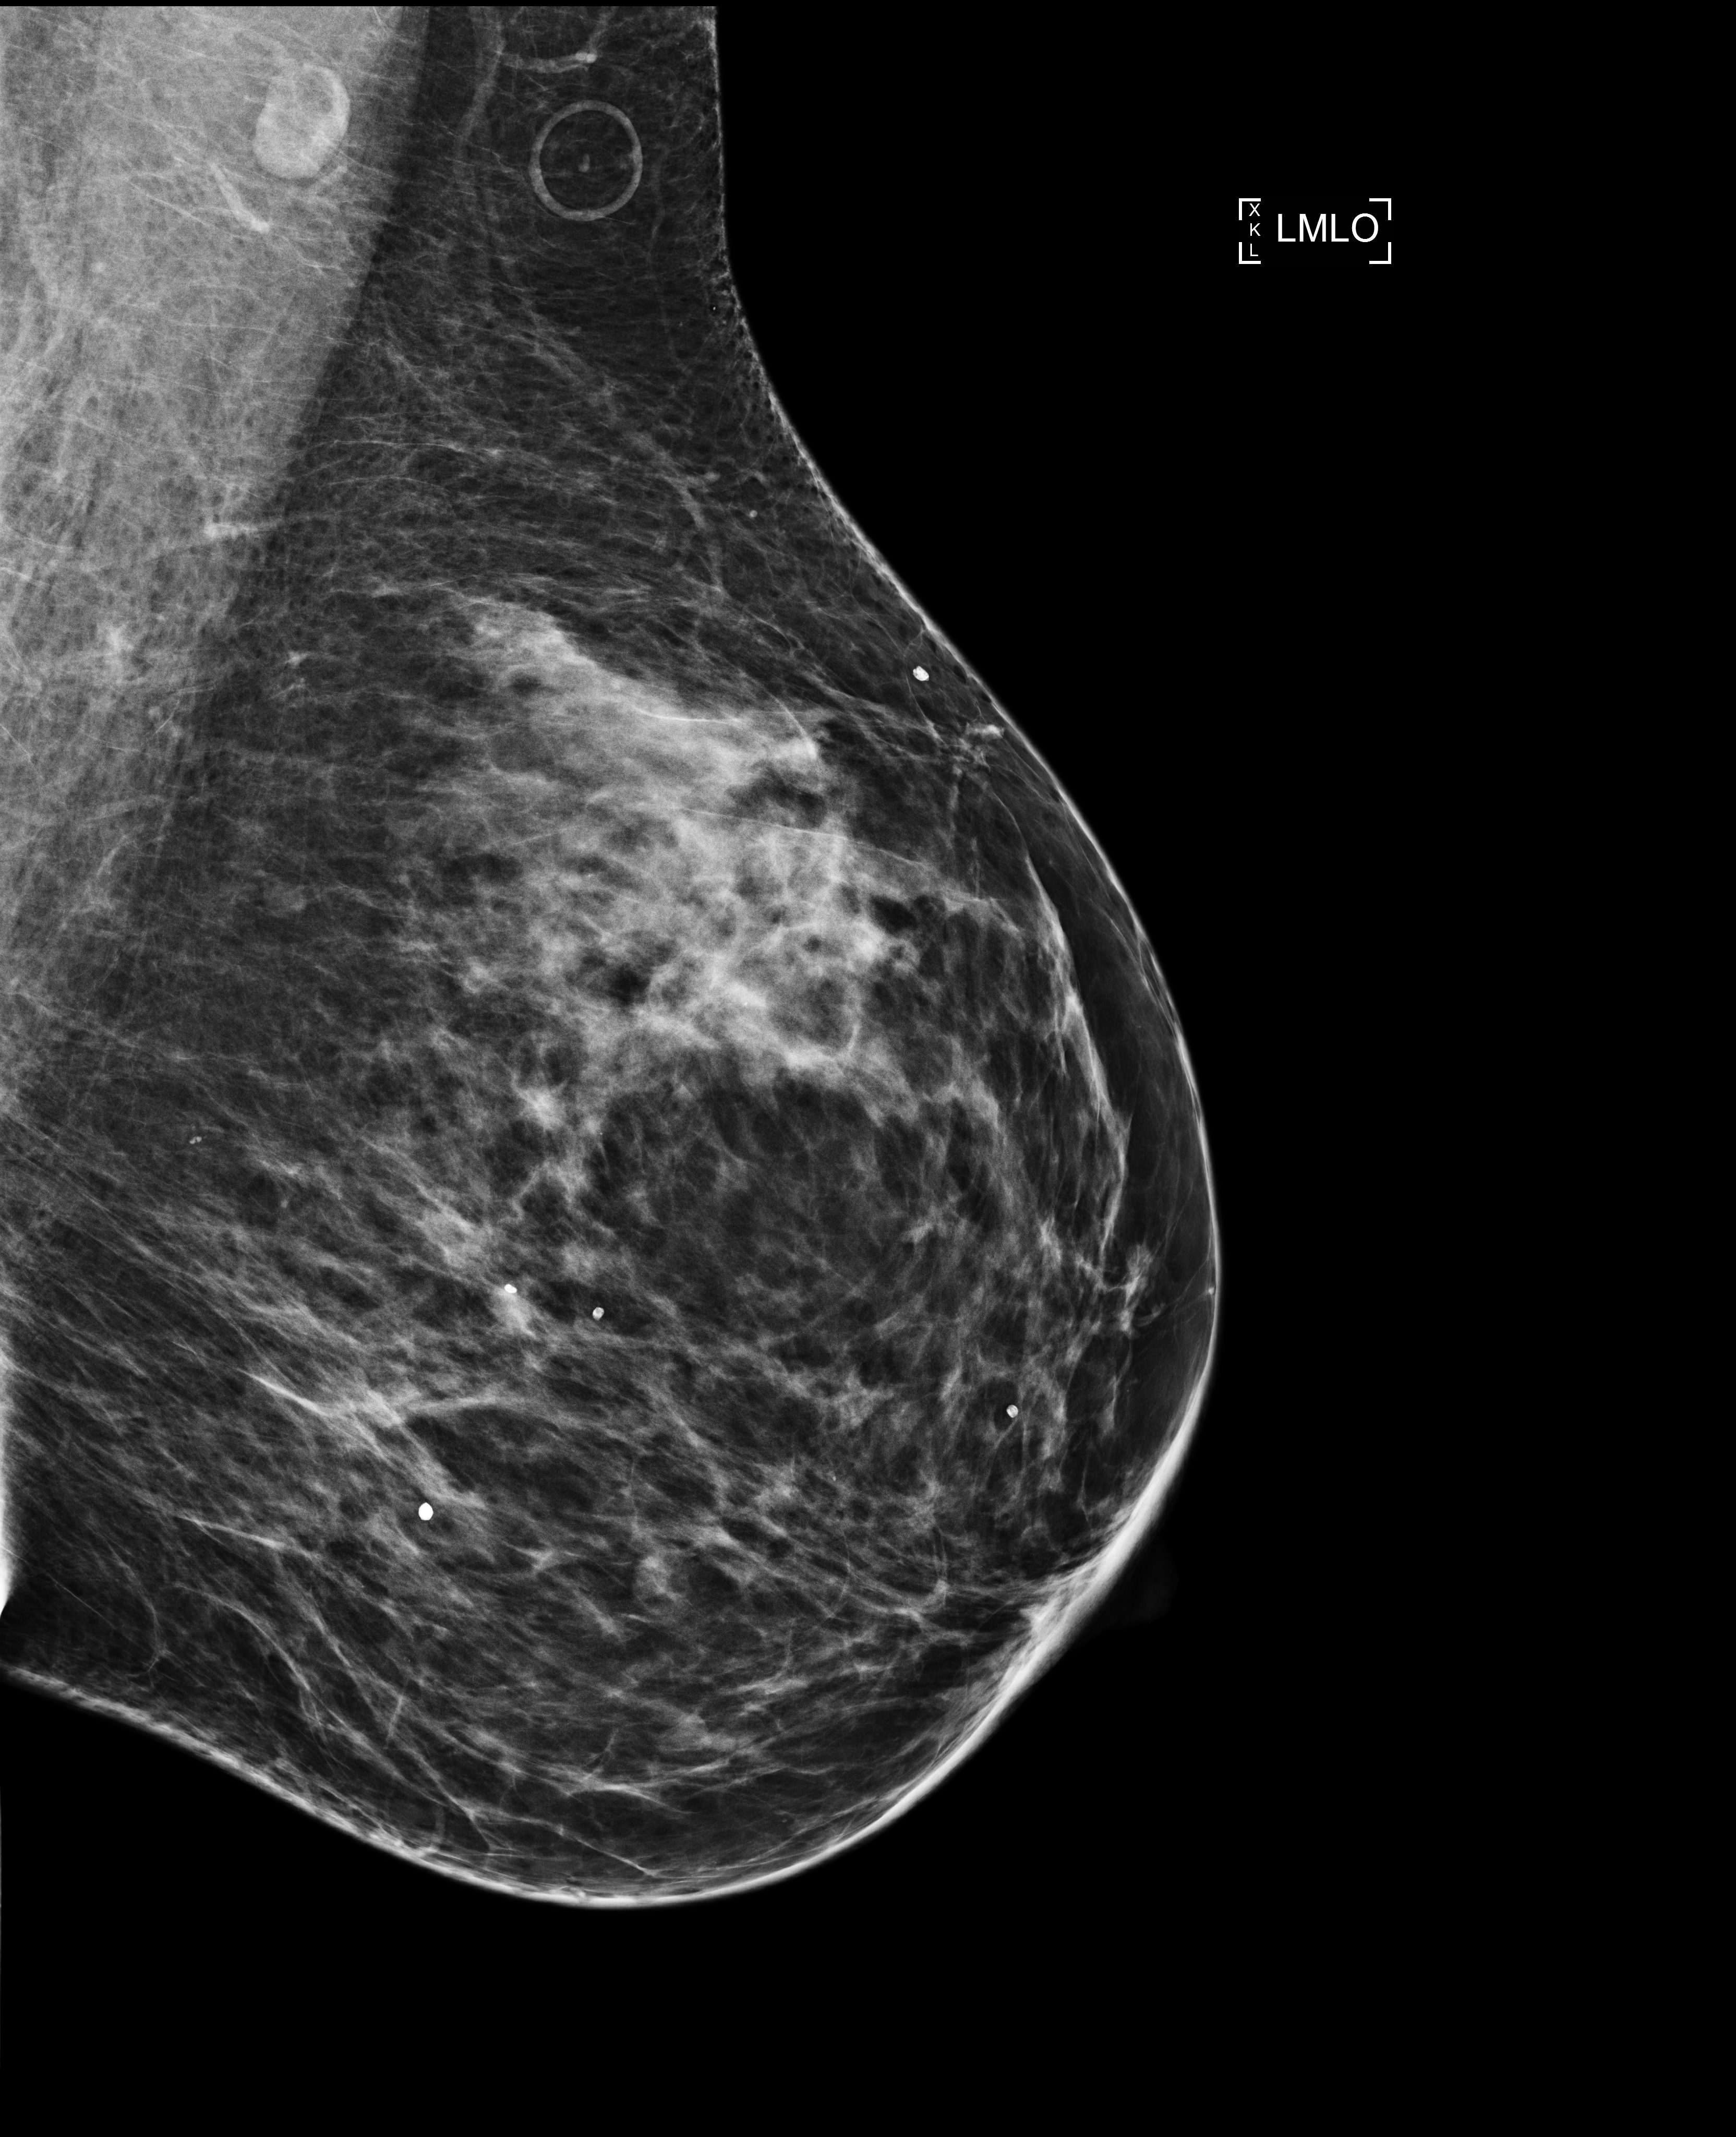
Annual screening mammography examination, compressed breast thickness 84 mm. Patient aged 46 years (female).
Image type: full-field digital mammogram. Breast: left. Projection: mediolateral oblique (MLO) view.